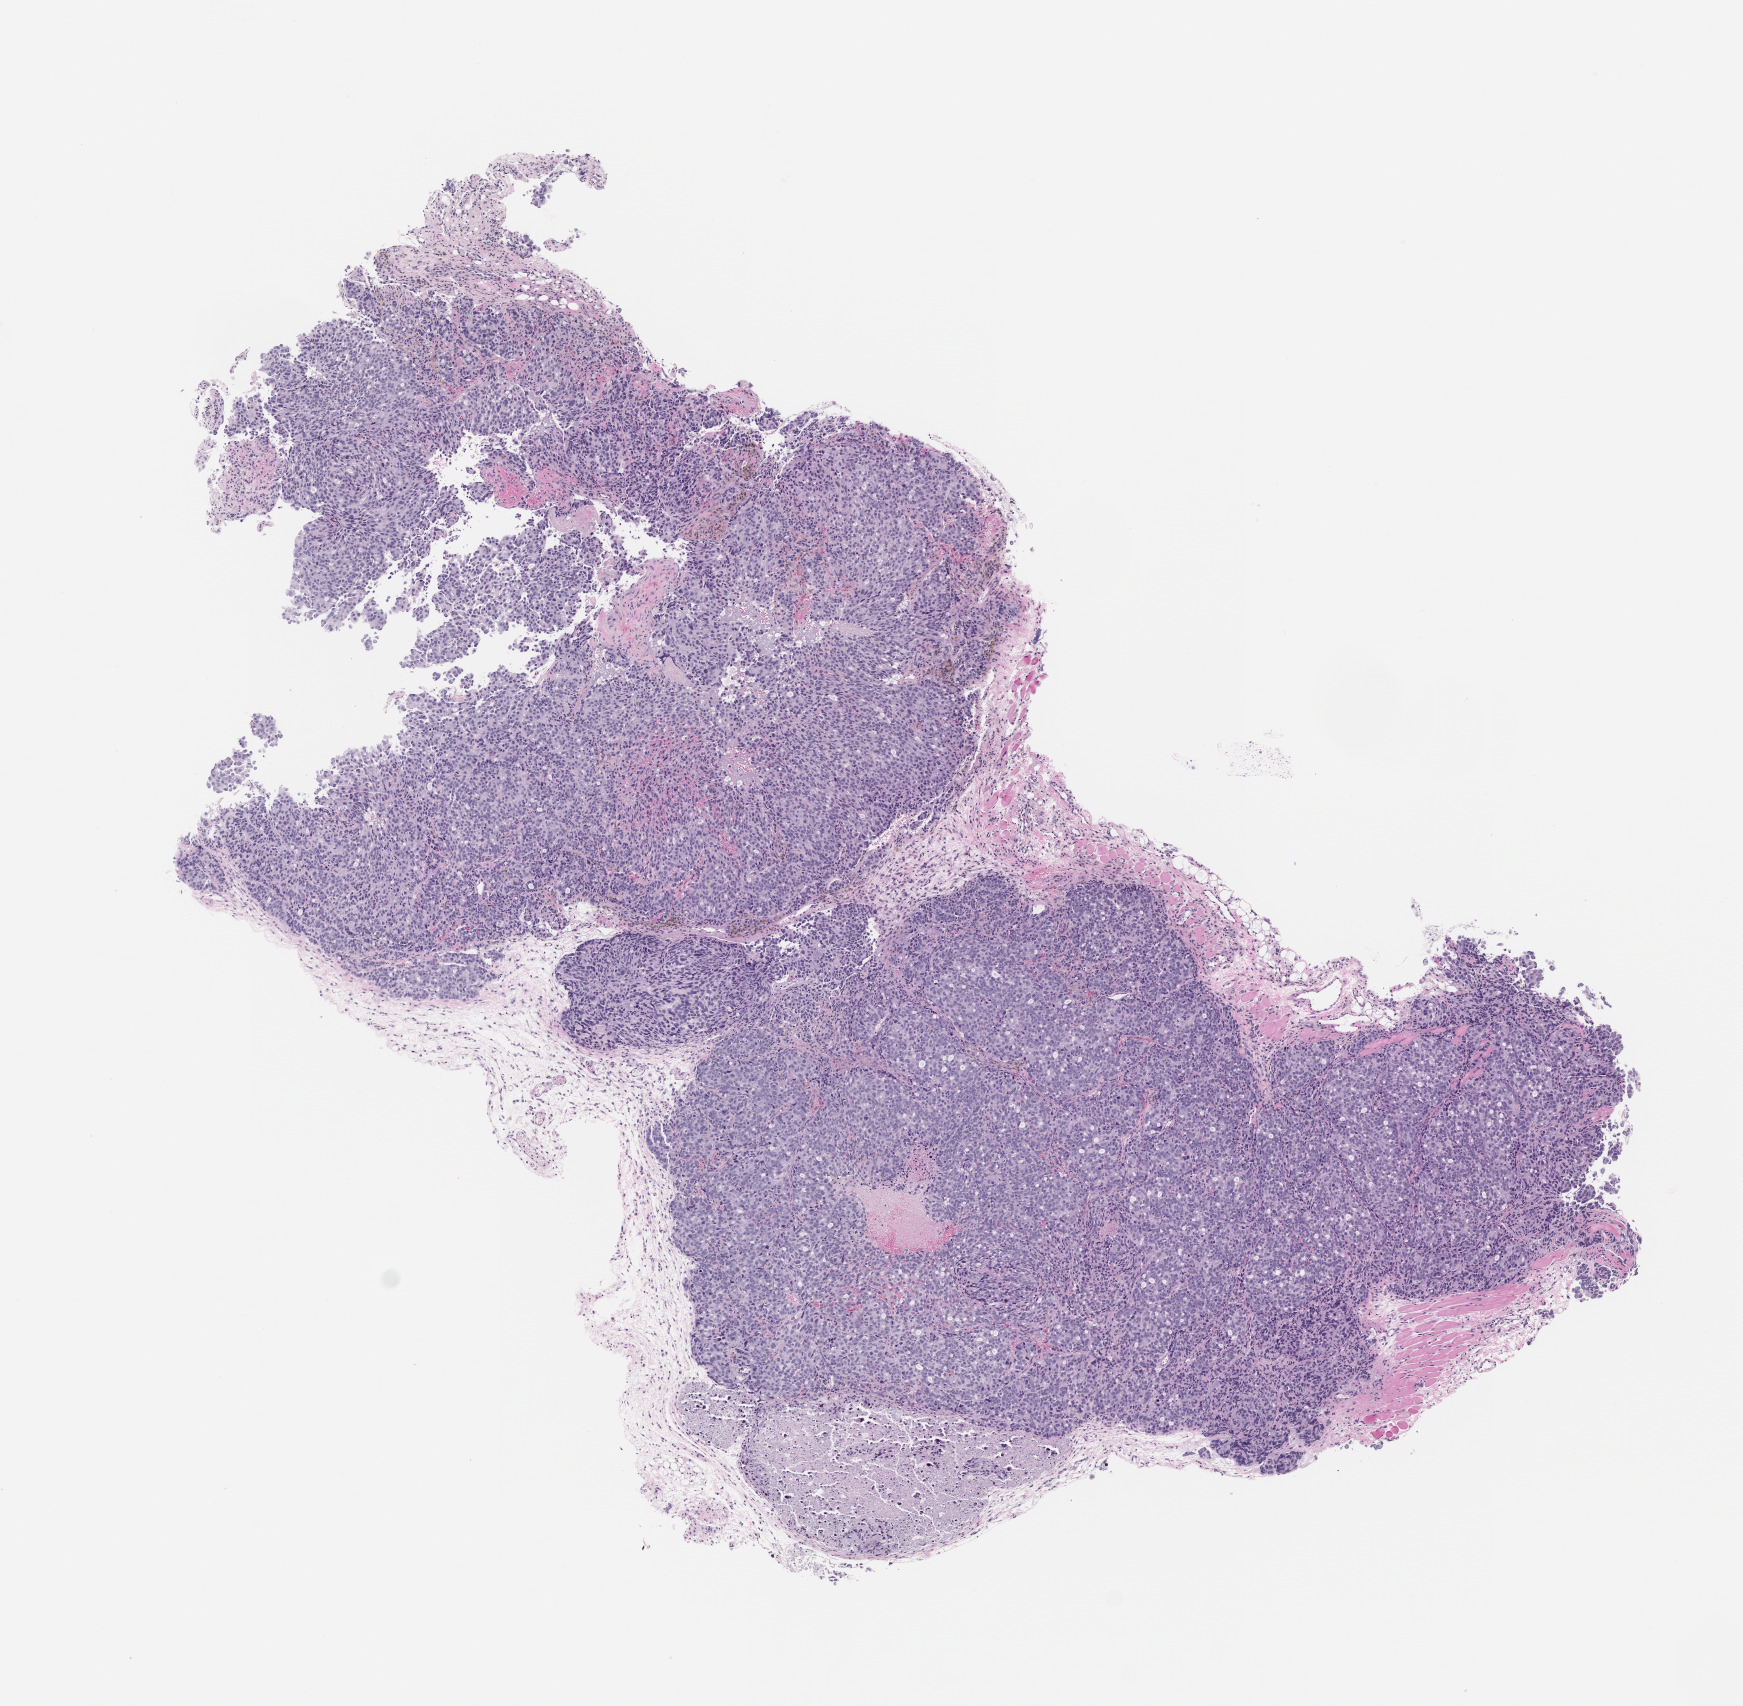
Whole-slide image, haematoxylin and eosin: patient-derived xenograft (human tumor grown in a mouse) — shown as a low-resolution overview of the whole scanned area (about 7.0 x 6.9 mm), formalin-fixed paraffin-embedded section, originating tumor site category: prostate.
* originating patient diagnosis: Prostate Carcinoma